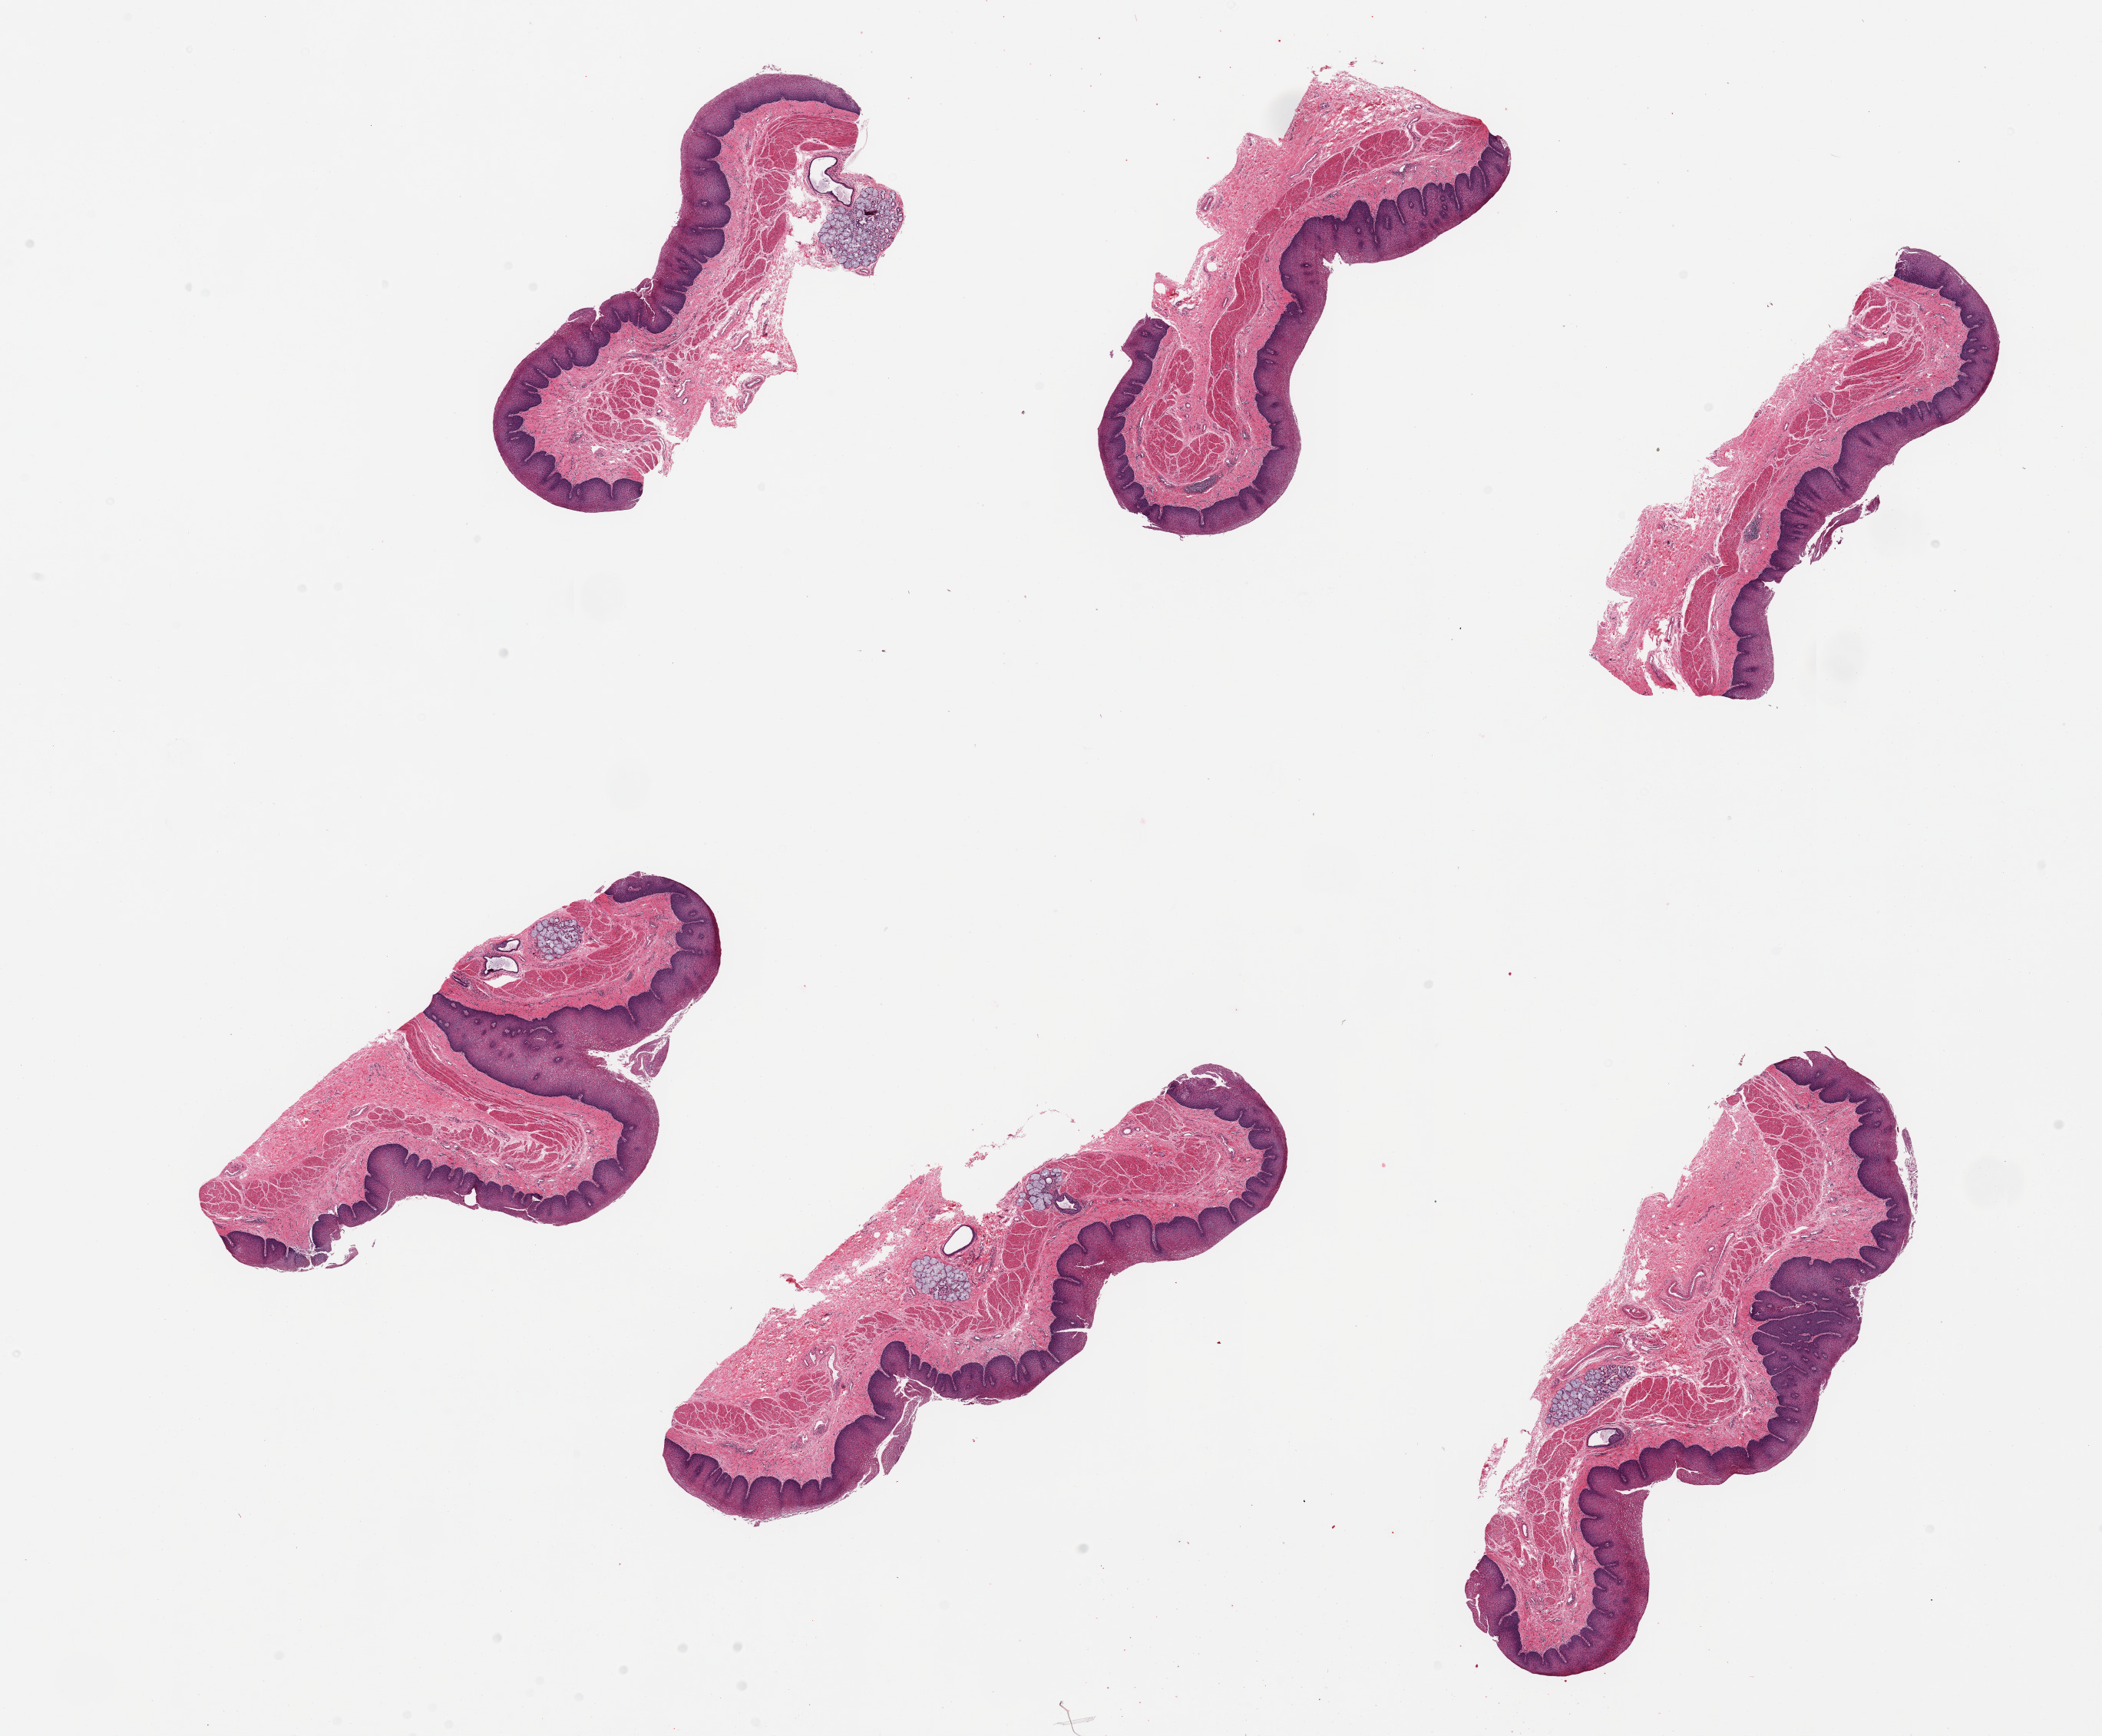
Whole-slide image, H&E stain, brightfield — shown as a low-resolution overview of the whole scanned area (about 21.7 x 17.9 mm), PAXgene-fixed, paraffin-embedded tissue, target tissue: esophageal mucous membrane, tissue donor sample. Donor sex: female.
* review note (as recorded): 6 pieces; well dissected; prominent submucosal glands